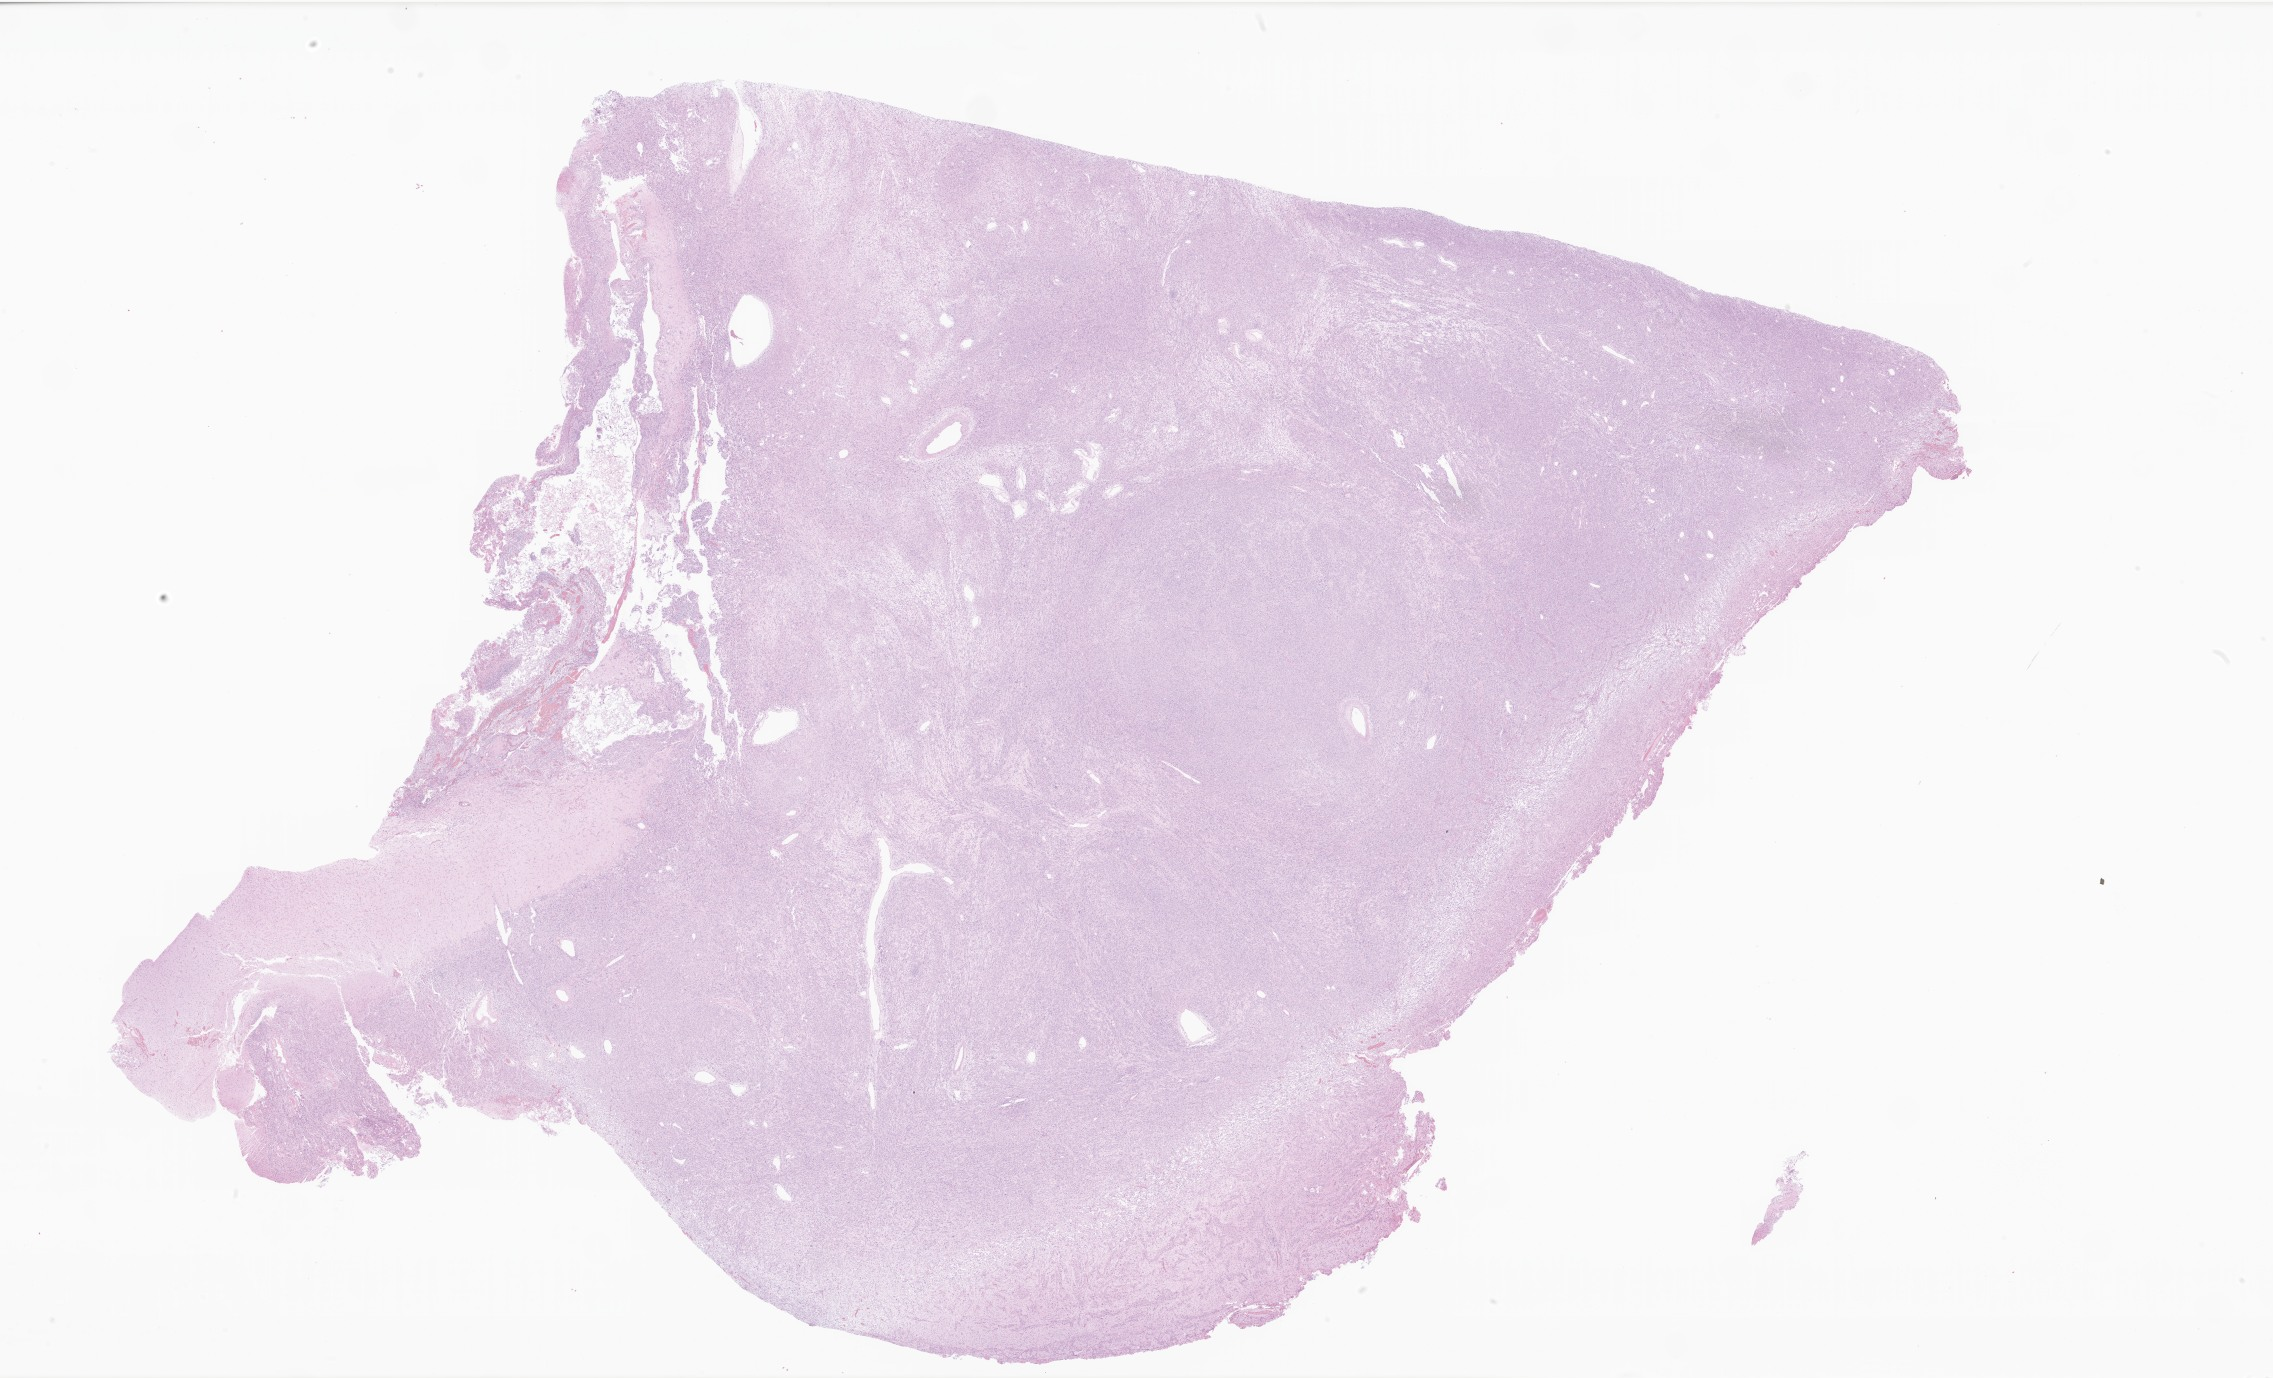
Whole-slide image, H&E stain of tumor tissue from the brain, shown as a low-resolution overview of the whole scanned area (about 38.3 x 23.2 mm), formalin-fixed paraffin-embedded section. Patient female; age 61 months (5 years 1 month).
Diagnosis (ICD-O-3 morphology term): Desmoplastic infantile astrocytoma.